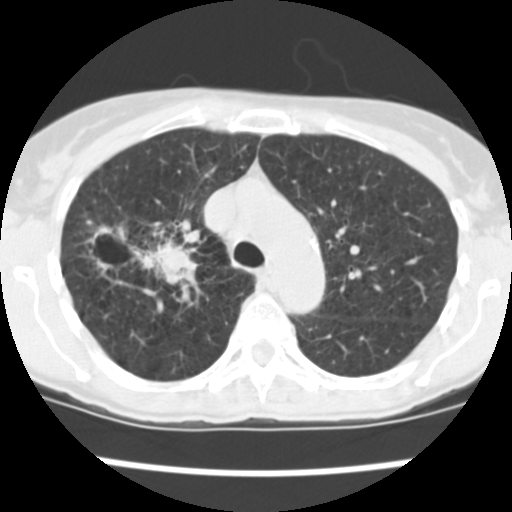
Chest CT (low-dose screening protocol), one axial image, baseline annual screen, lung window (W 1500 / L -600 HU), 2.5 mm slice thickness, standard (soft-tissue) reconstruction kernel (STANDARD), 120 kVp, slice 176 of 252 in the series, 512 × 512 image matrix. Female, age 60 years at enrolment. Current smoker at enrolment.
Lesion marked by an expert reader, box from (x=84, y=216) to (x=199, y=285) px. The screening reader recorded 3 non-calcified nodules or masses ≥4 mm on this exam (right upper lobe, right upper lobe, right lower lobe); which of them this box marks is not recorded. Lung cancer was diagnosed 19 days after this screen: non-small cell carcinoma, right upper lobe, stage IV (AJCC 6th edition), 26 mm at pathology.